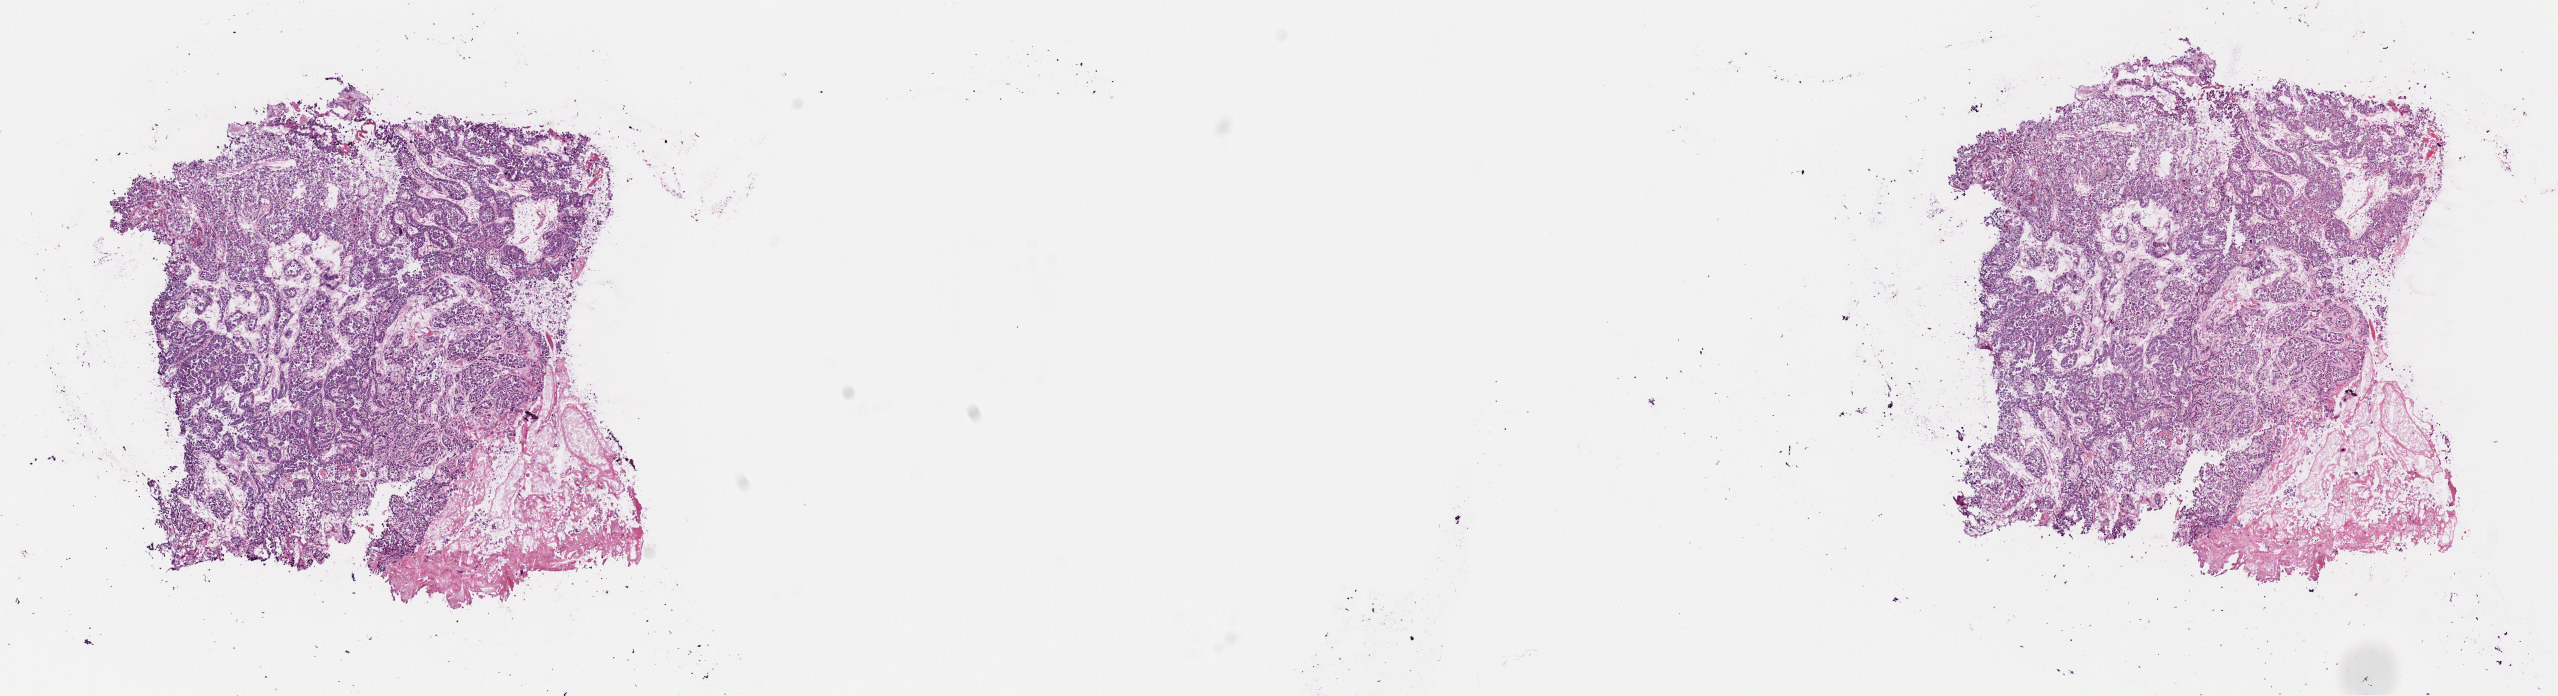
H&E whole-slide image, low-resolution overview of the scanned area, about 20.2 x 5.5 mm; frozen section; uterus, primary tumour sample. Patient: female, age at initial diagnosis 61 years. Histologic grade: G3 (poorly differentiated). Slide review estimates, as recorded: tumour cells 80%, tumour nuclei 80%, normal cells 0%, stromal cells 5%, necrosis 15%. Infiltration values recorded for this section: lymphocyte infiltration 40%, monocyte infiltration 10%, neutrophil infiltration 30%.
• histologic diagnosis: Serous cystadenocarcinoma, NOS (endometrium)
• FIGO stage: IVB